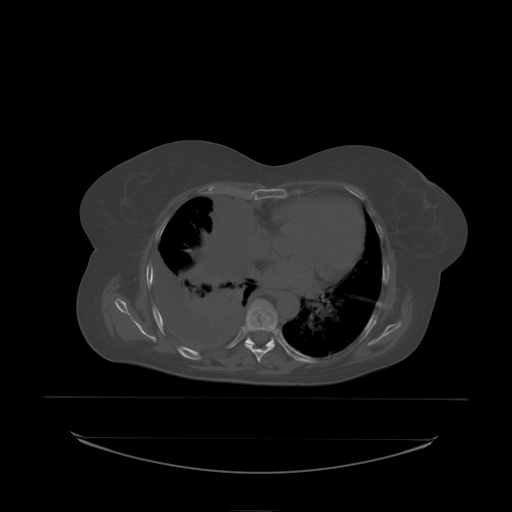
CT including the spine, one axial slice. Position 138 of 242 along the scan axis. Bone window (W 1800 / L 400 HU). 2.5 mm slice thickness. 512 × 512 image matrix, field of view 500 × 500 mm. Female patient, age 53 years. From the clinical record (not read from this slice): primary cancer: lung; vertebrae with lytic lesions (as recorded): T7, L1.
Annotated regions visible in this slice (semi-automatically segmented with operator editing):
- T7 vertebra: bounding box <246,300,278,333> (left, top, right, bottom; pixels)
- T8 vertebra: <254,301,278,331>